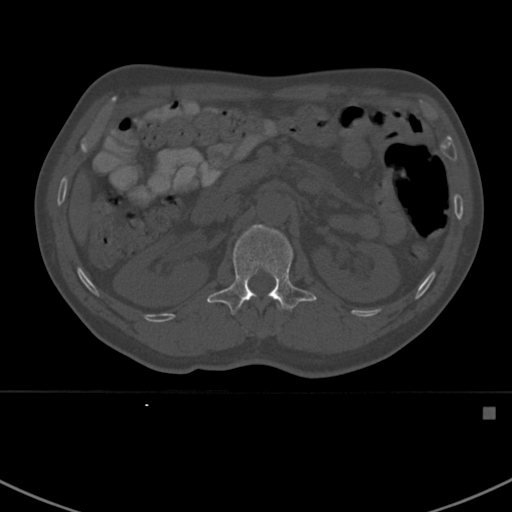
CT including the spine, one axial slice. Position 311 of 412 along the scan axis. Reconstruction kernel Br40s. Bone window (W 1800 / L 400 HU). 1.5 mm slice thickness. 512 × 512 image matrix, field of view 358 × 358 mm. Male patient, age 59 years. From the clinical record (not read from this slice): primary cancer: prostate.
Structures marked on this image (semi-automatically segmented with operator editing):
- L1 vertebra: bounding box [x1, y1, x2, y2] px = [207, 224, 317, 315]